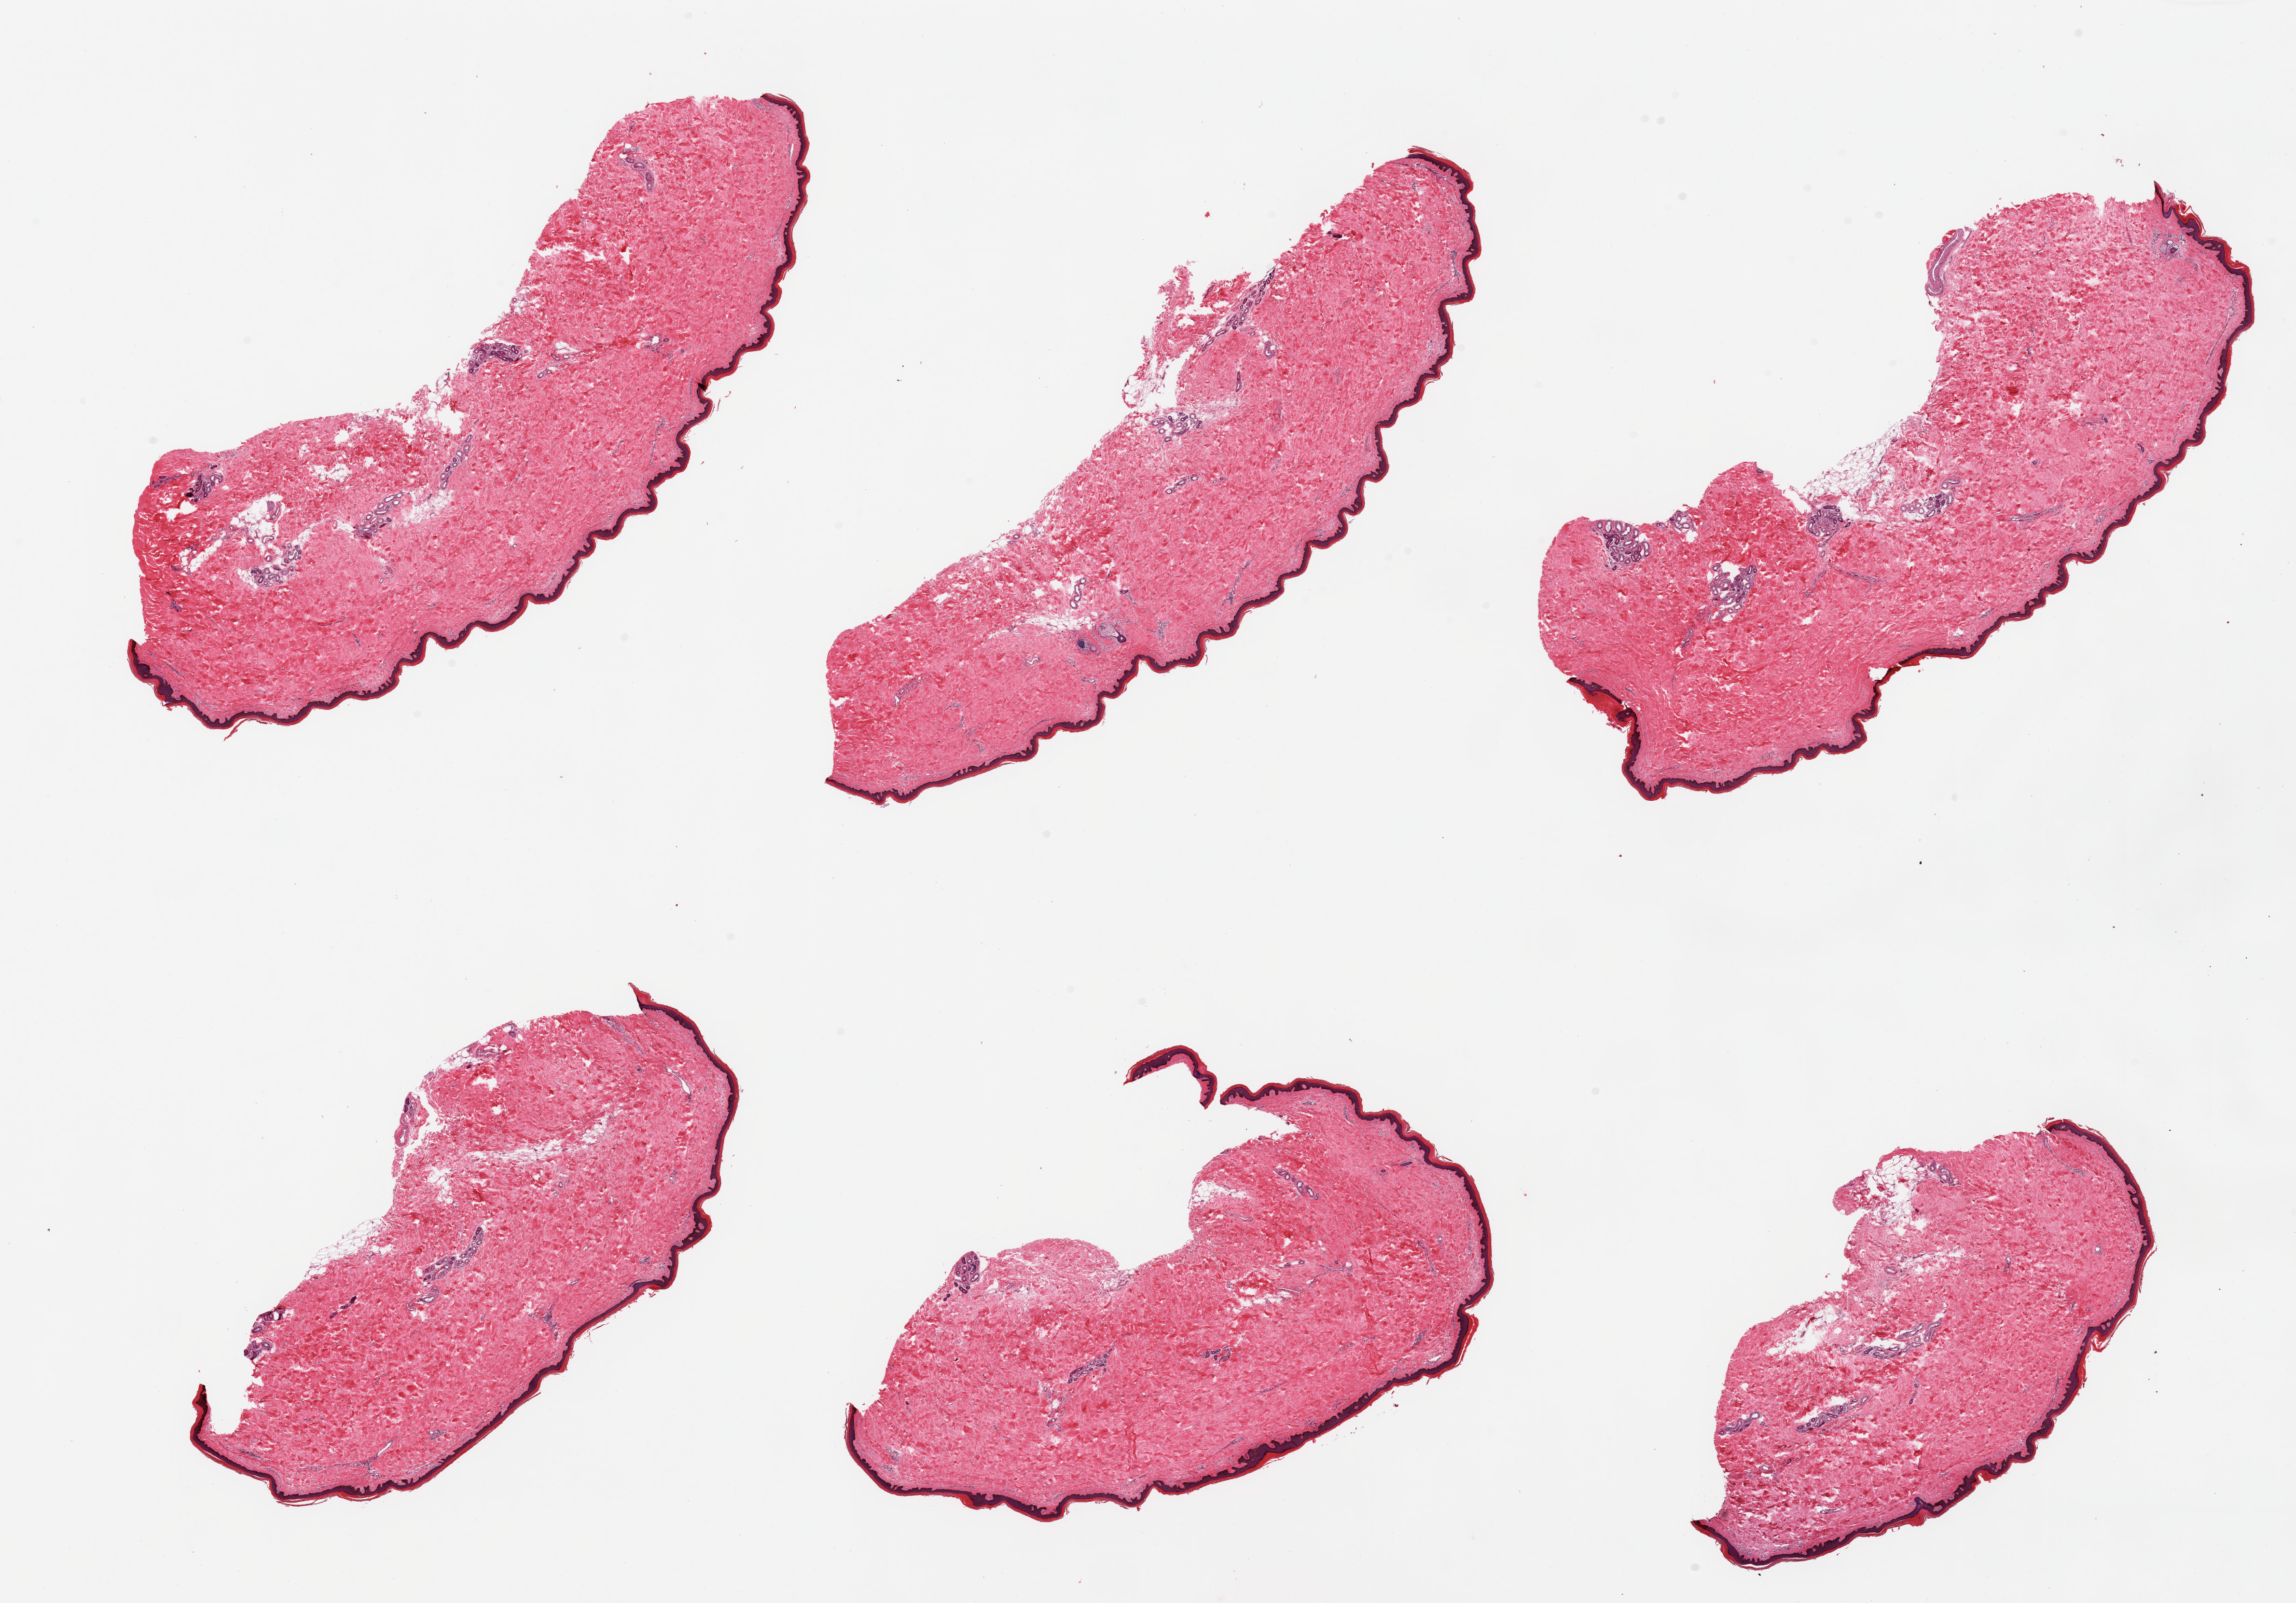
Whole-slide image, H&E stain — low-resolution overview of the scanned area, about 26.6 x 18.6 mm (slide scanned at 20x), PAXgene-fixed, paraffin-embedded tissue, target tissue: skin of lower leg, tissue donor sample. Male donor.
• pathologist's review note for this sample: 6 pieces; well dissected; 5% dermal fat